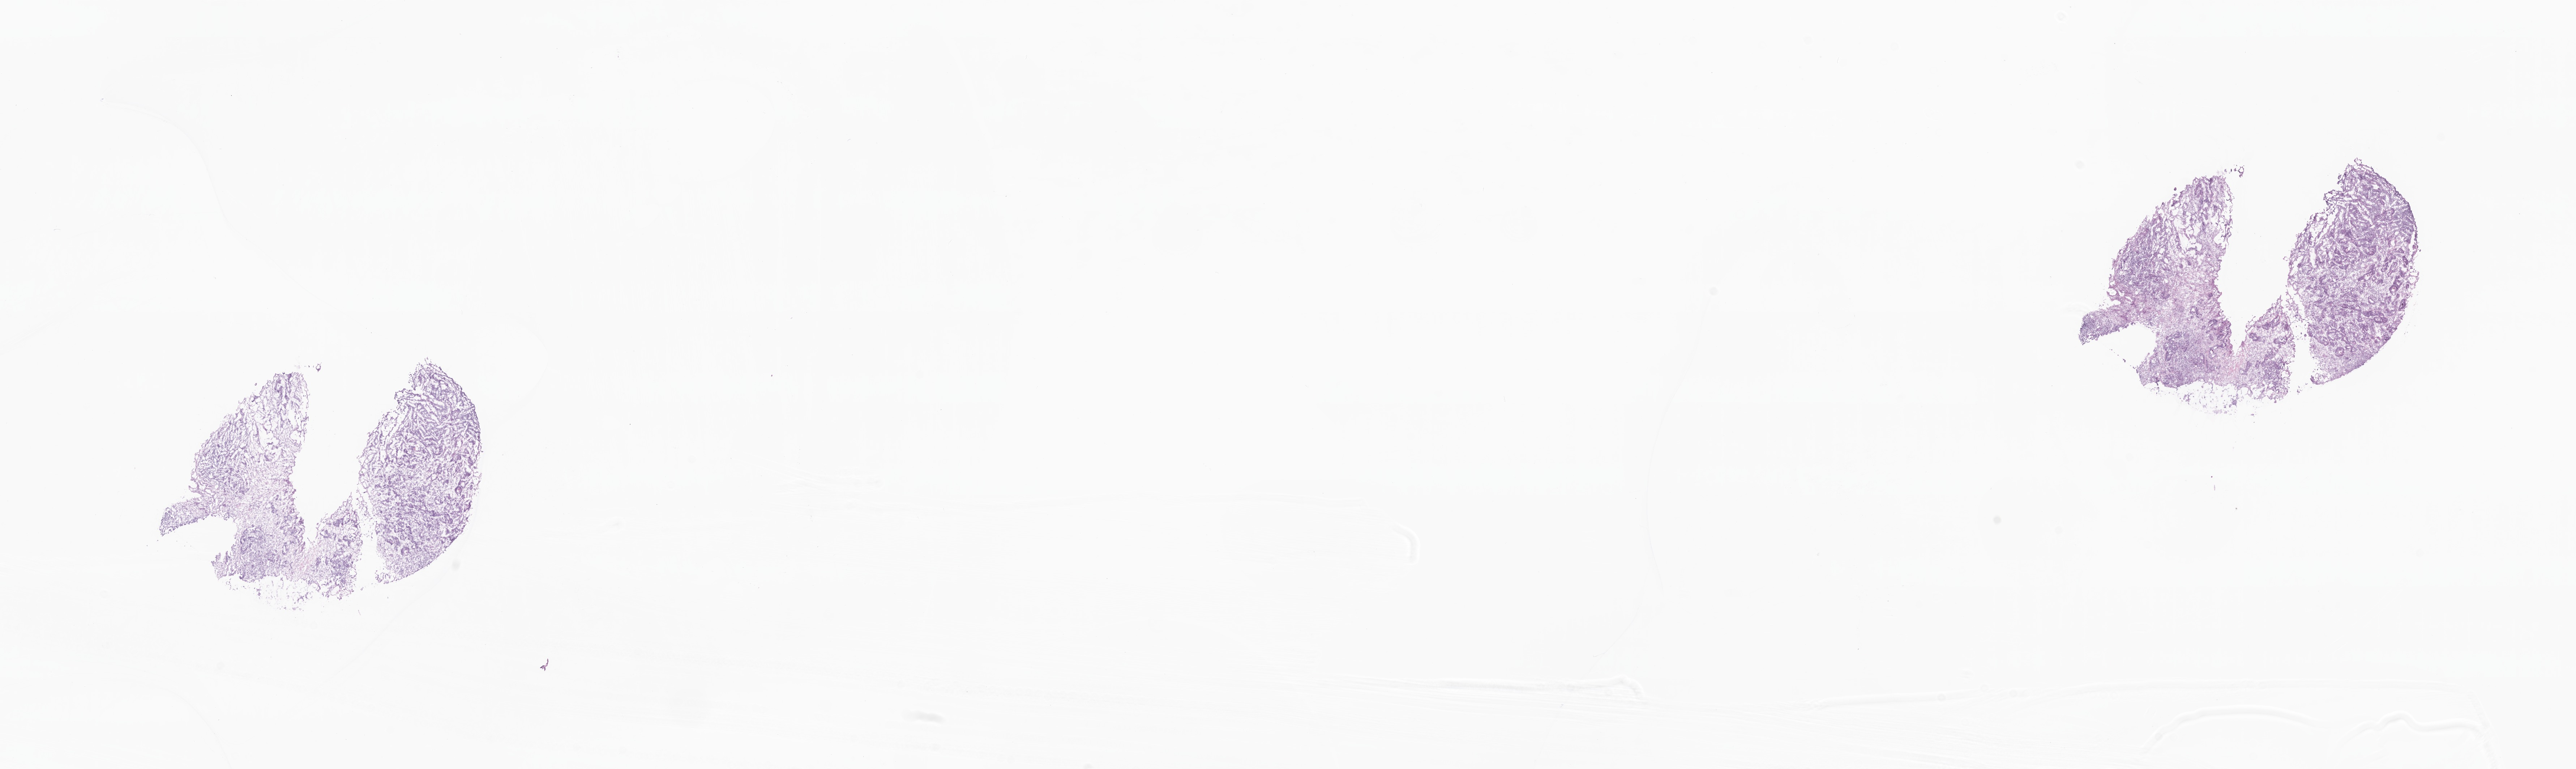
Digitized haematoxylin and eosin-stained section, a low-resolution overview of the entire scanned area, about 30.0 x 9.0 mm. Frozen section (tissue freezing medium). Metastatic tumor tissue, resected from liver. Male patient; age at initial diagnosis 53 years. Slide review estimates, as recorded: tumor cells 50%, tumor nuclei 50%, stromal cells 30%, necrosis 5%, normal cells 15%. Infiltration values recorded for this section: lymphocyte infiltration 10%, monocyte infiltration 2%, neutrophil infiltration 2%.
* patient diagnosis (primary): Adenocarcinoma, NOS